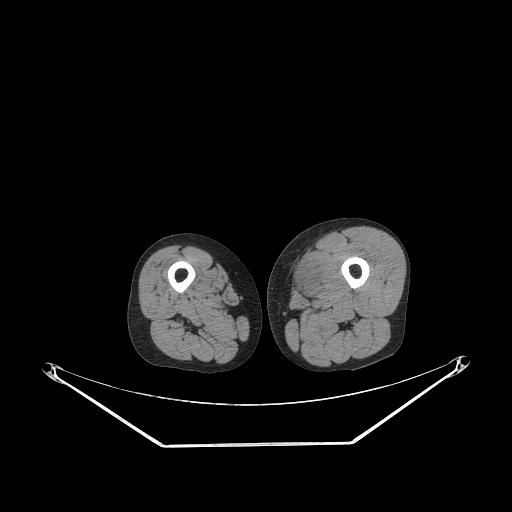
CT of an extremity soft-tissue mass (from a PET/CT study), one axial slice. Position 226 of 267 along the scan axis. 140 kVp. Soft-tissue window (W 400 / L 40 HU). 3.75 mm slice thickness. 512 × 512 image matrix, field of view 500 × 500 mm. Male patient. From the clinical record (not read from this slice): histological type: pleiomorphic leiomyosarcoma; grade: high; site of the primary tumour: left thigh.
Annotated regions visible in this slice (expert contour drawn on MRI and transferred to this co-registered scan by the dataset authors):
- gross tumour volume including surrounding oedema: bounding box <288,251,327,293> (left, top, right, bottom; pixels)
- gross tumour volume (mass): <292,258,318,291>